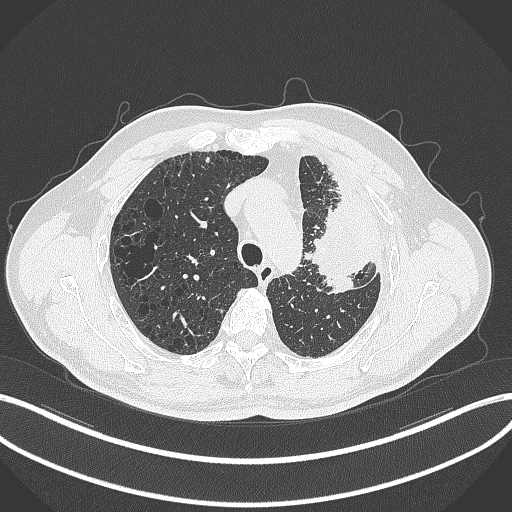
Chest CT, one axial slice; position 242 of 297 along the scan axis; lung window (W 1500 / L -600 HU); 1 mm slice thickness; 512 × 512 image matrix, field of view 400 × 400 mm. Male patient, age 68 years. From the clinical record (not read from this slice): clinical TNM (as recorded): T3 N3 M1.
Annotated regions visible in this slice (rectangle marked by the reading radiologist):
- lung tumour (recorded histology: adenocarcinoma): bounding box <310,191,364,303> (left, top, right, bottom; pixels)